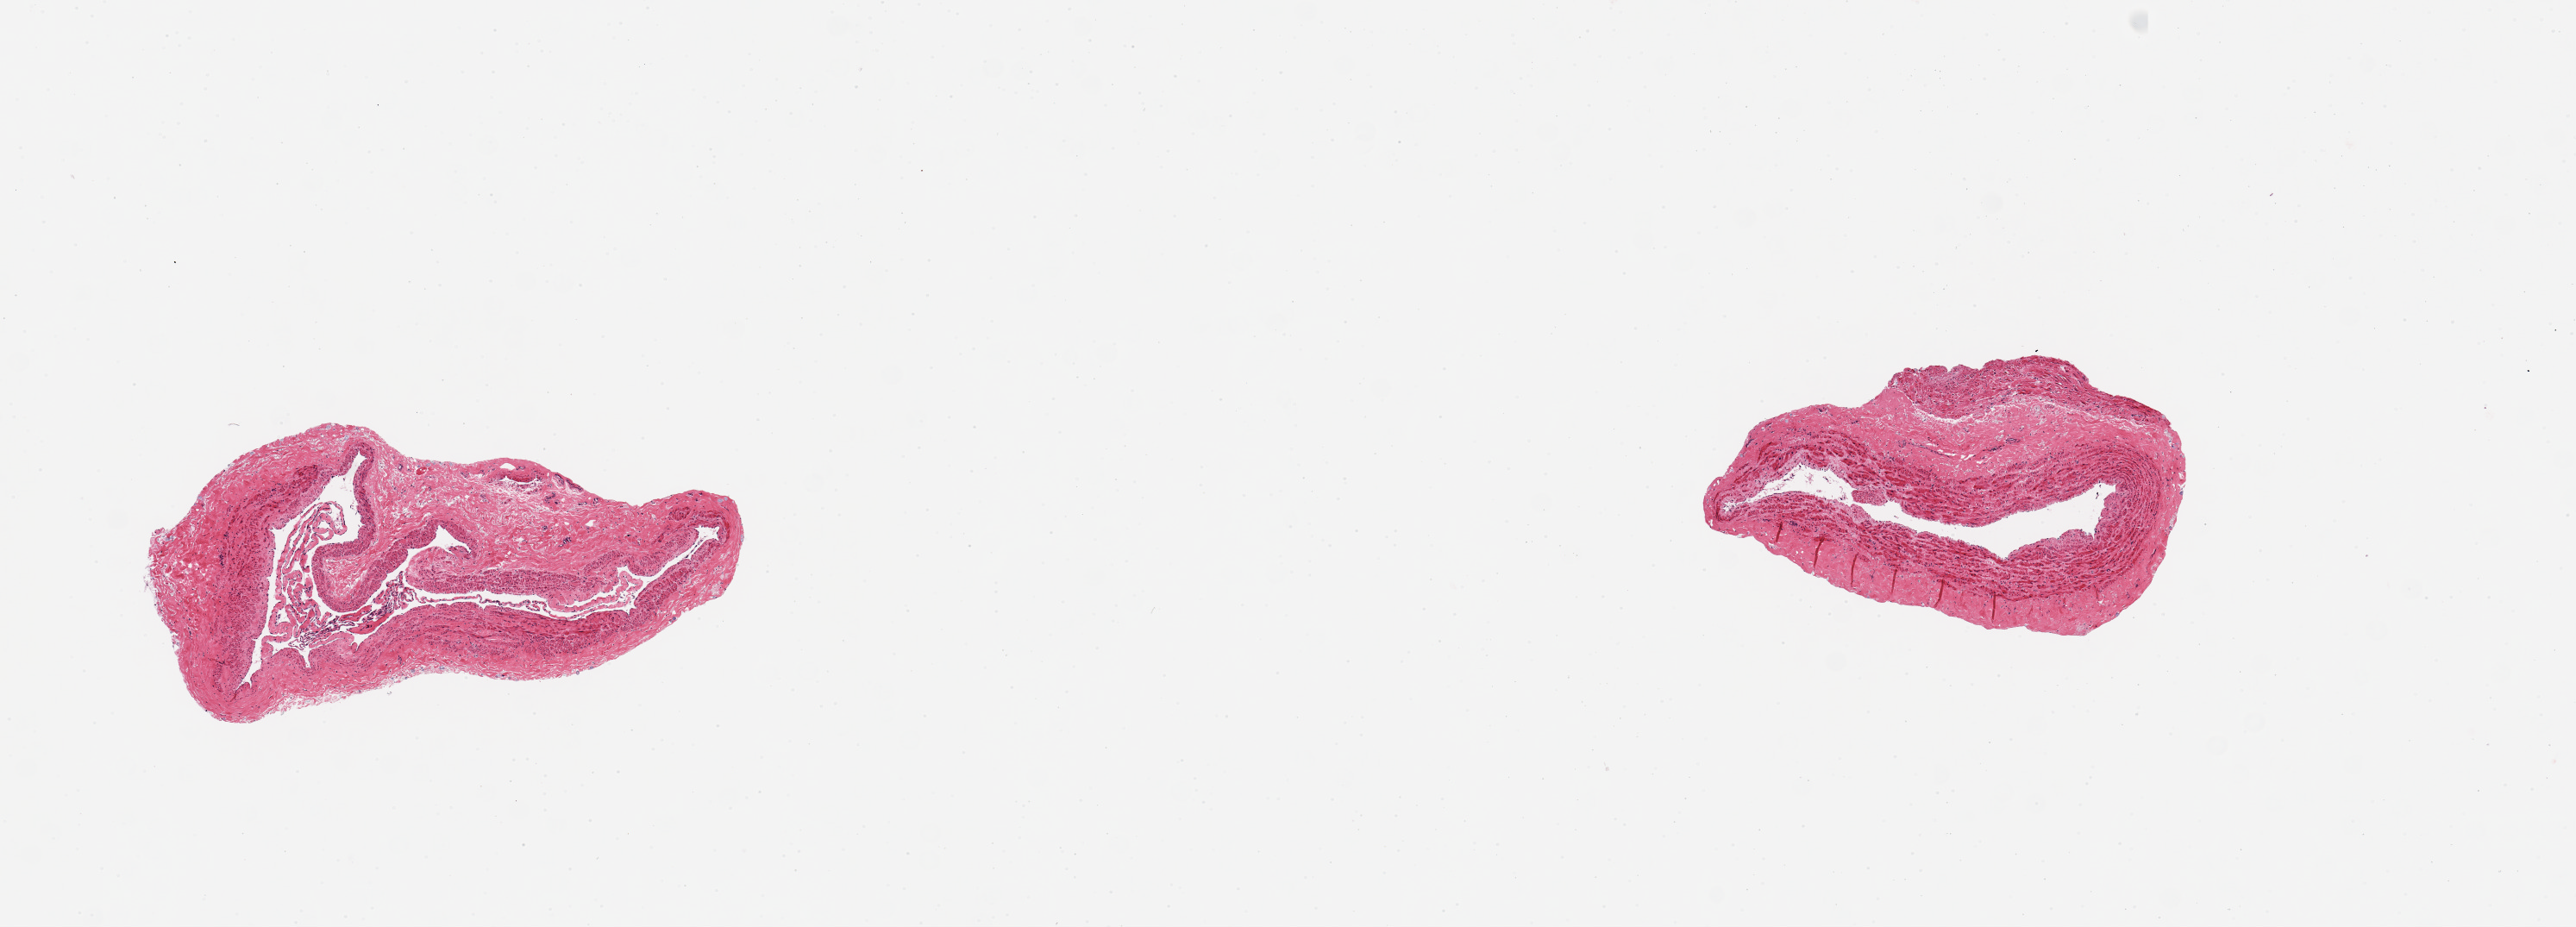
Hematoxylin and eosin (H&E) whole-slide image, brightfield, a low-resolution overview of the entire scanned area, about 11.8 x 4.3 mm, PAXgene-fixed paraffin-embedded (PFPE) section, section of tibial artery (target tissue), donor tissue sample. Donor sex: female.
Review note (as recorded): 2 pieces ~1.5-2mm d. Good clean specimens, minimal atherosclerosis.